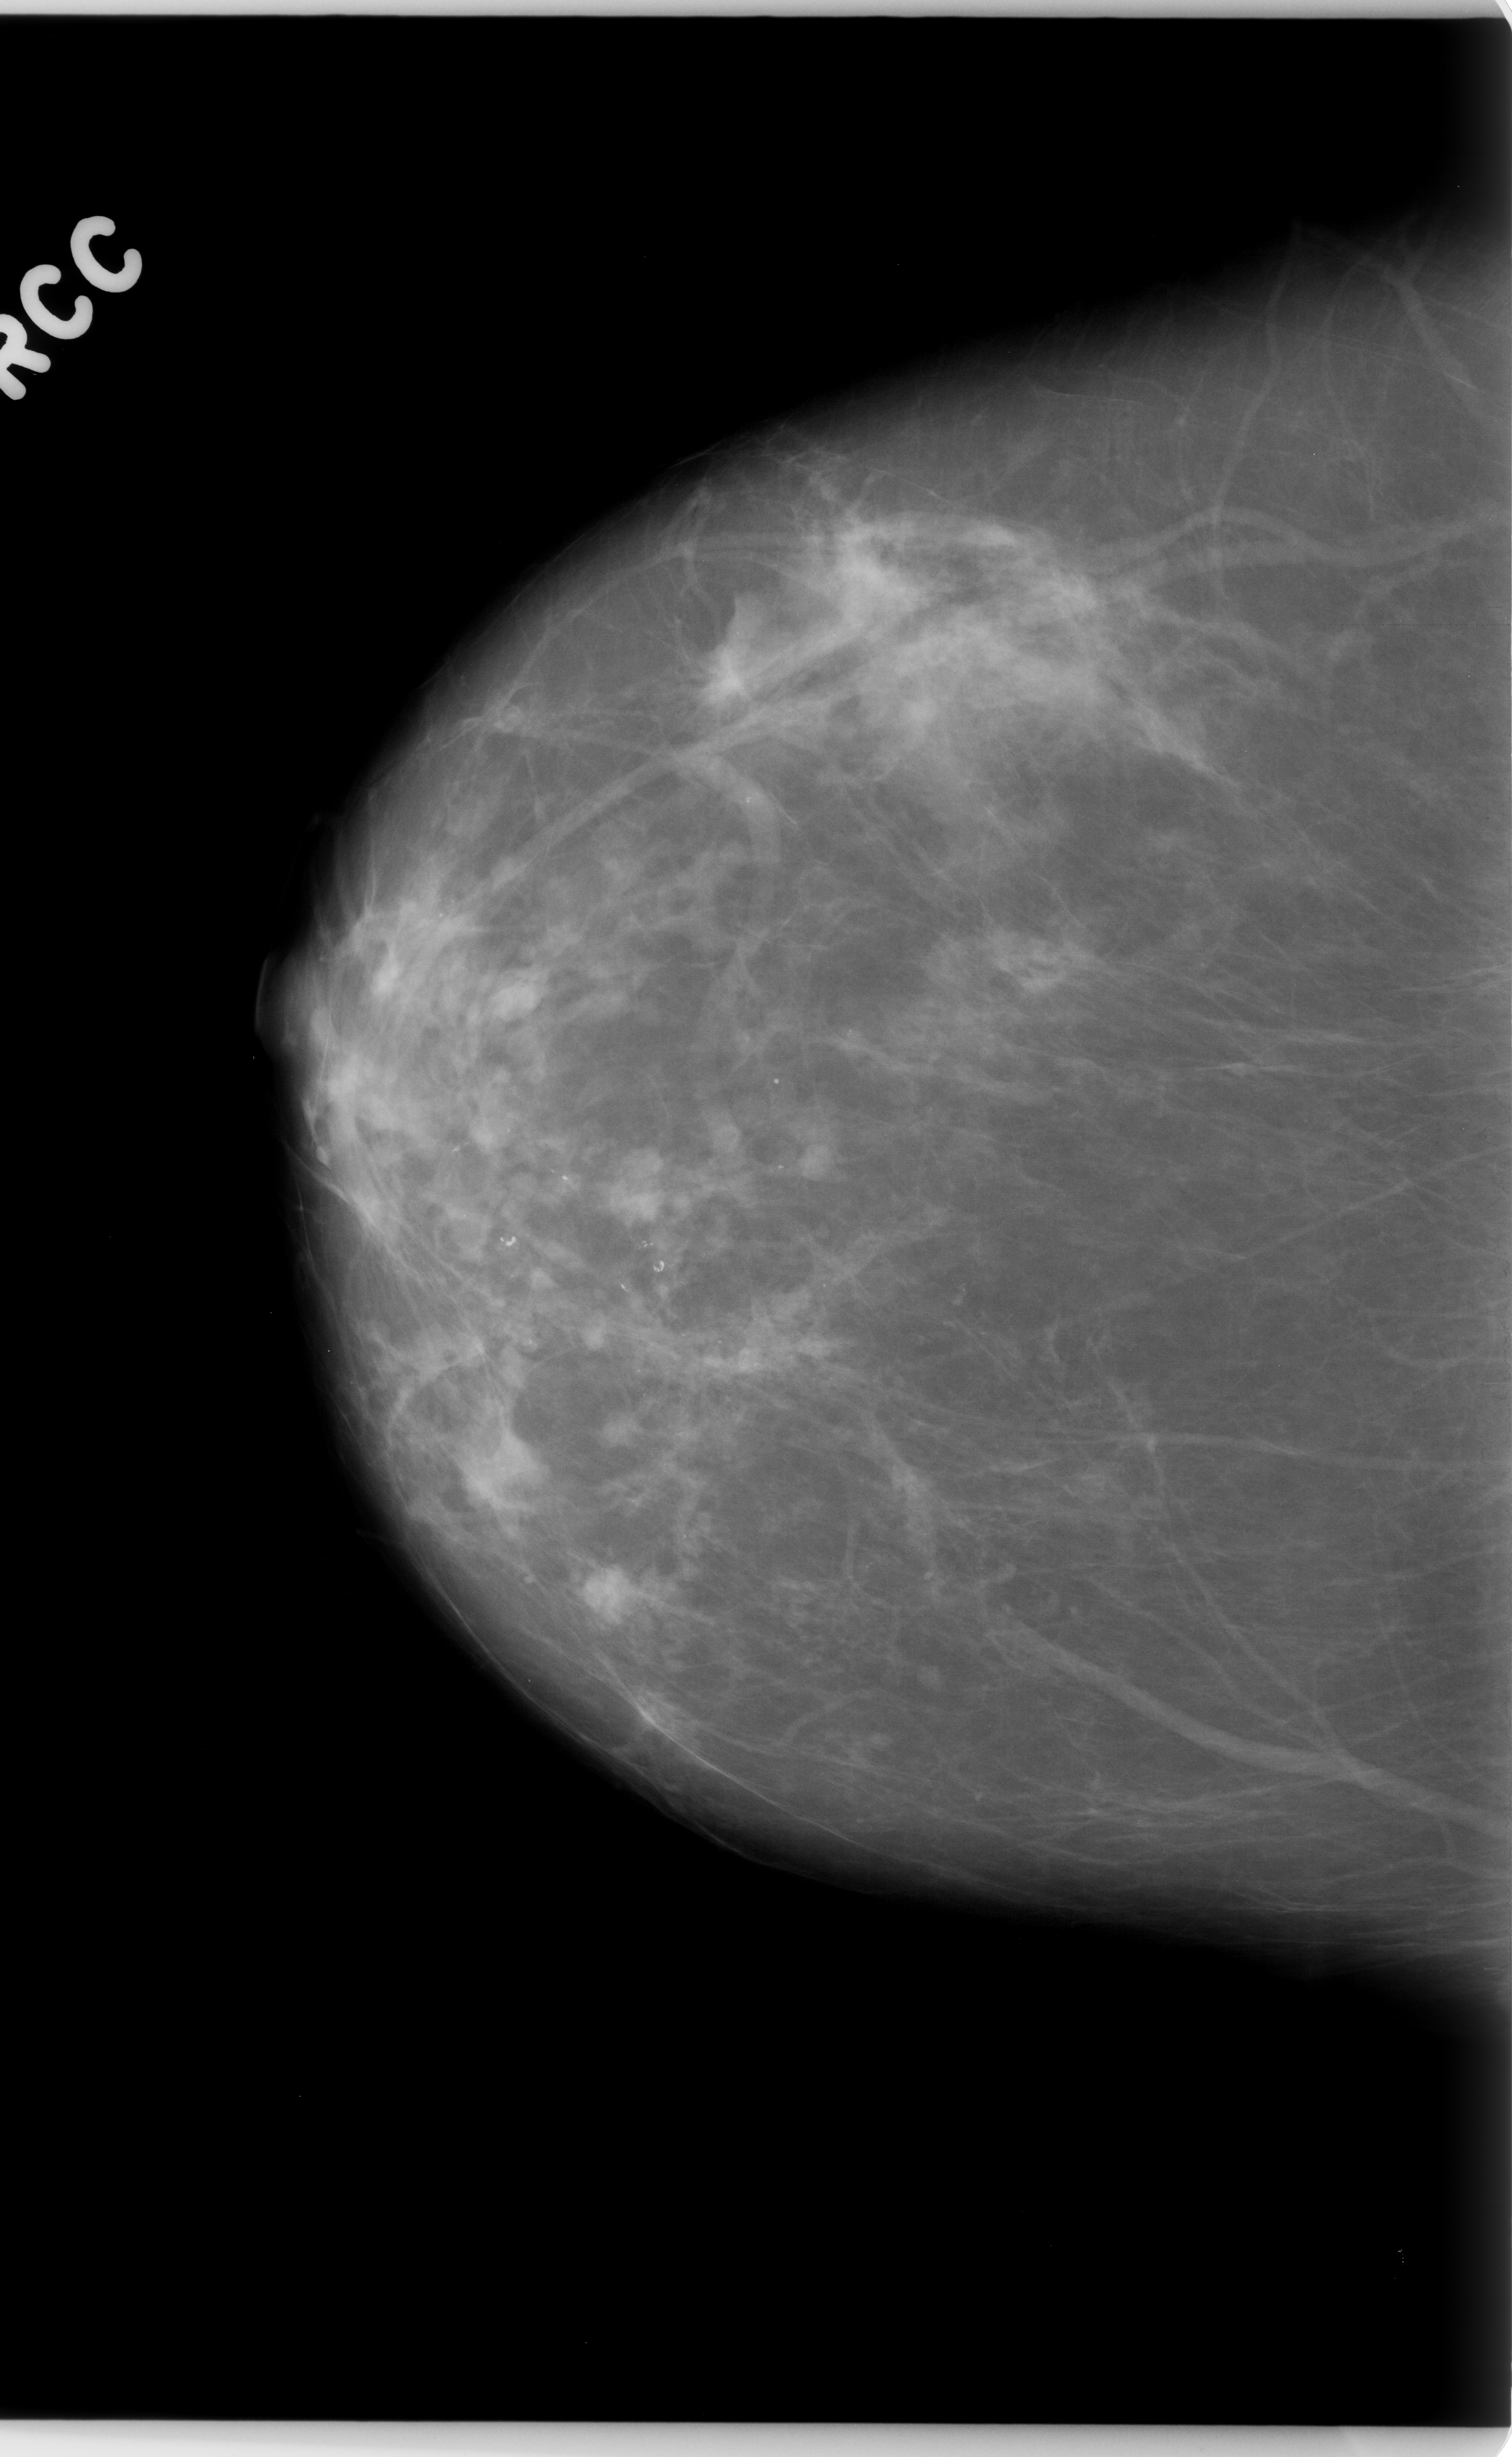
Mammogram (digitized film); right breast; CC view; breast composition: scattered fibroglandular densities (BI-RADS density category 2 of 4); 1512 × 2457 image matrix.
Expert-marked regions of interest on this film, with their recorded descriptors:
- calcifications, morphology pleomorphic, distribution segmental; BI-RADS assessment category 4; subtlety rating 4 on a 1 (subtle) to 5 (obvious) scale; pathology result (as recorded, not read from the image): malignant: bounding box [x1, y1, x2, y2] px = [393, 1101, 1079, 1577]